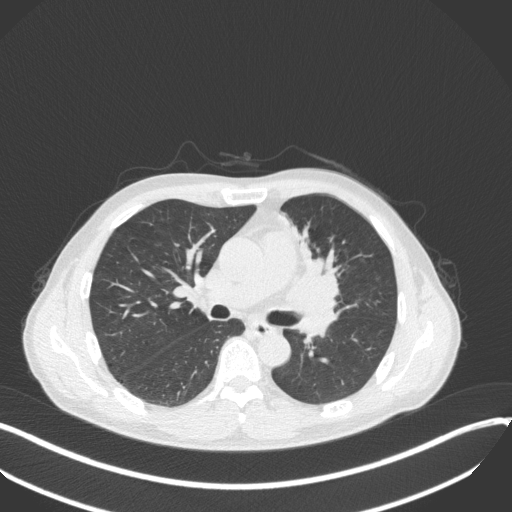
Chest CT, one axial slice; slice 196 of 411 in the series (ordered by position); lung window (W 1500 / L -600 HU); 1 mm slice thickness; 512 × 512 image matrix, field of view 400 × 400 mm. Patient: male, 56 years. Case-level facts recorded for this patient, not image findings: clinical TNM (as recorded): T2a N0 M0.
Structures marked on this image (bounding box drawn by a radiologist):
- lung tumour (recorded histology: squamous cell carcinoma): bounding box (x1, y1, x2, y2) in pixels: (286, 236, 348, 308)